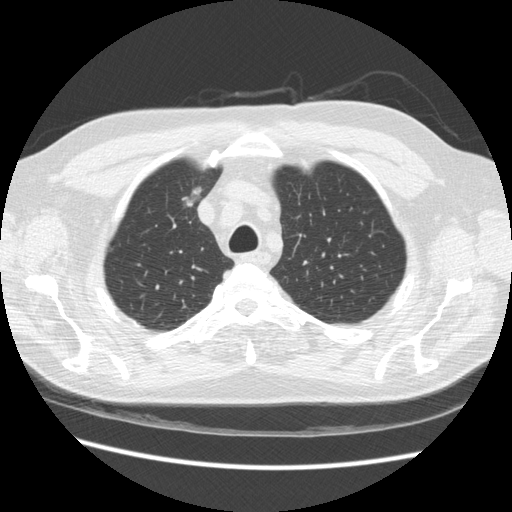
Low-dose screening chest CT, one axial slice. Slice 185 of 234 in the series (ordered by position). Reconstruction kernel STANDARD. 120 kVp. Lung window (W 1500 / L -600 HU). 512 × 512 image matrix.
Outlined on this slice (manually delineated by an expert):
- lesion 1 (tumor, upper lobe of right lung): box from (x=182, y=186) to (x=201, y=206) px